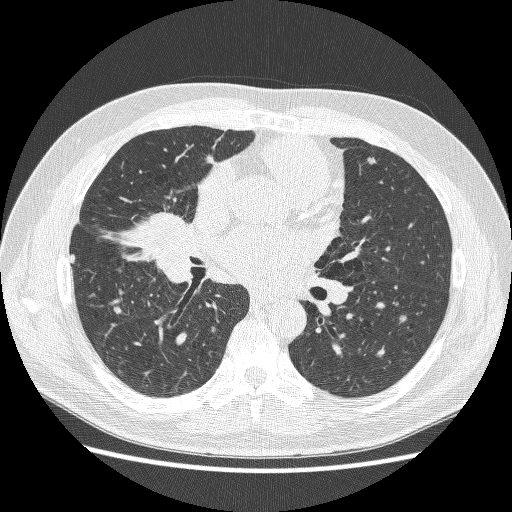
Low-dose screening chest CT, axial slice, baseline screening round, lung window (W 1500 / L -600 HU), 1.25 mm slice thickness, 120 kVp, 512 × 512 image matrix, field of view 360 × 360 mm. Male participant, aged 59 years at enrolment. Former smoker at enrolment.
Expert-annotated lung lesion, bounding box (x1, y1, x2, y2) in pixels: (124, 196, 197, 266). No non-calcified nodule or mass ≥4 mm was recorded by the screening reader at this exam. Official screen result: positive, change unspecified: nodule(s) >= 4 mm or enlarging nodule(s), mass(es), or other non-specific abnormalities suspicious for lung cancer. Participant outcome: lung cancer diagnosed 24 days after this screen — adenocarcinoma, NOS, right middle lobe, poorly differentiated (G3), stage IV (AJCC 6th edition), 54 mm at pathology.